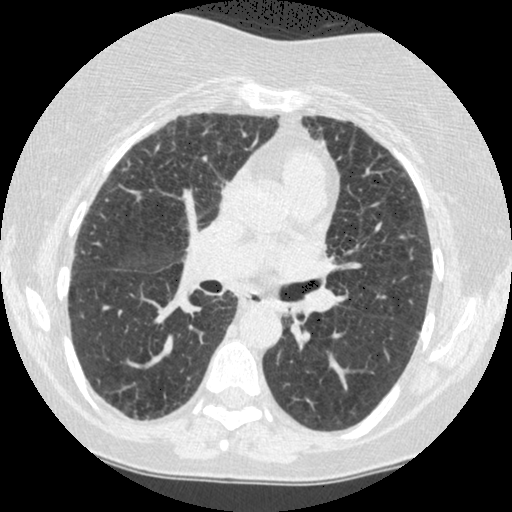
Axial slice from a low-dose chest CT screening exam, baseline annual screen, lung window (W 1500 / L -600 HU), standard (soft-tissue) reconstruction kernel (STANDARD), slice 200 of 442 in the series, 512 × 512 image matrix, field of view 310 × 310 mm. Female participant, aged 60 years at enrolment. Former smoker at enrolment.
• Expert reader's lesion annotation, bounding box [x1, y1, x2, y2] px = [272, 295, 312, 337].
• The screening reader recorded 2 non-calcified nodules or masses ≥4 mm on this exam (right lower lobe, left lower lobe); which of them this box marks is not recorded.
• Participant outcome: lung cancer diagnosed 794 days after this screen — small cell carcinoma, NOS, left lower lobe, undifferentiated (G4), stage IV (AJCC 6th edition), 69 mm at pathology.